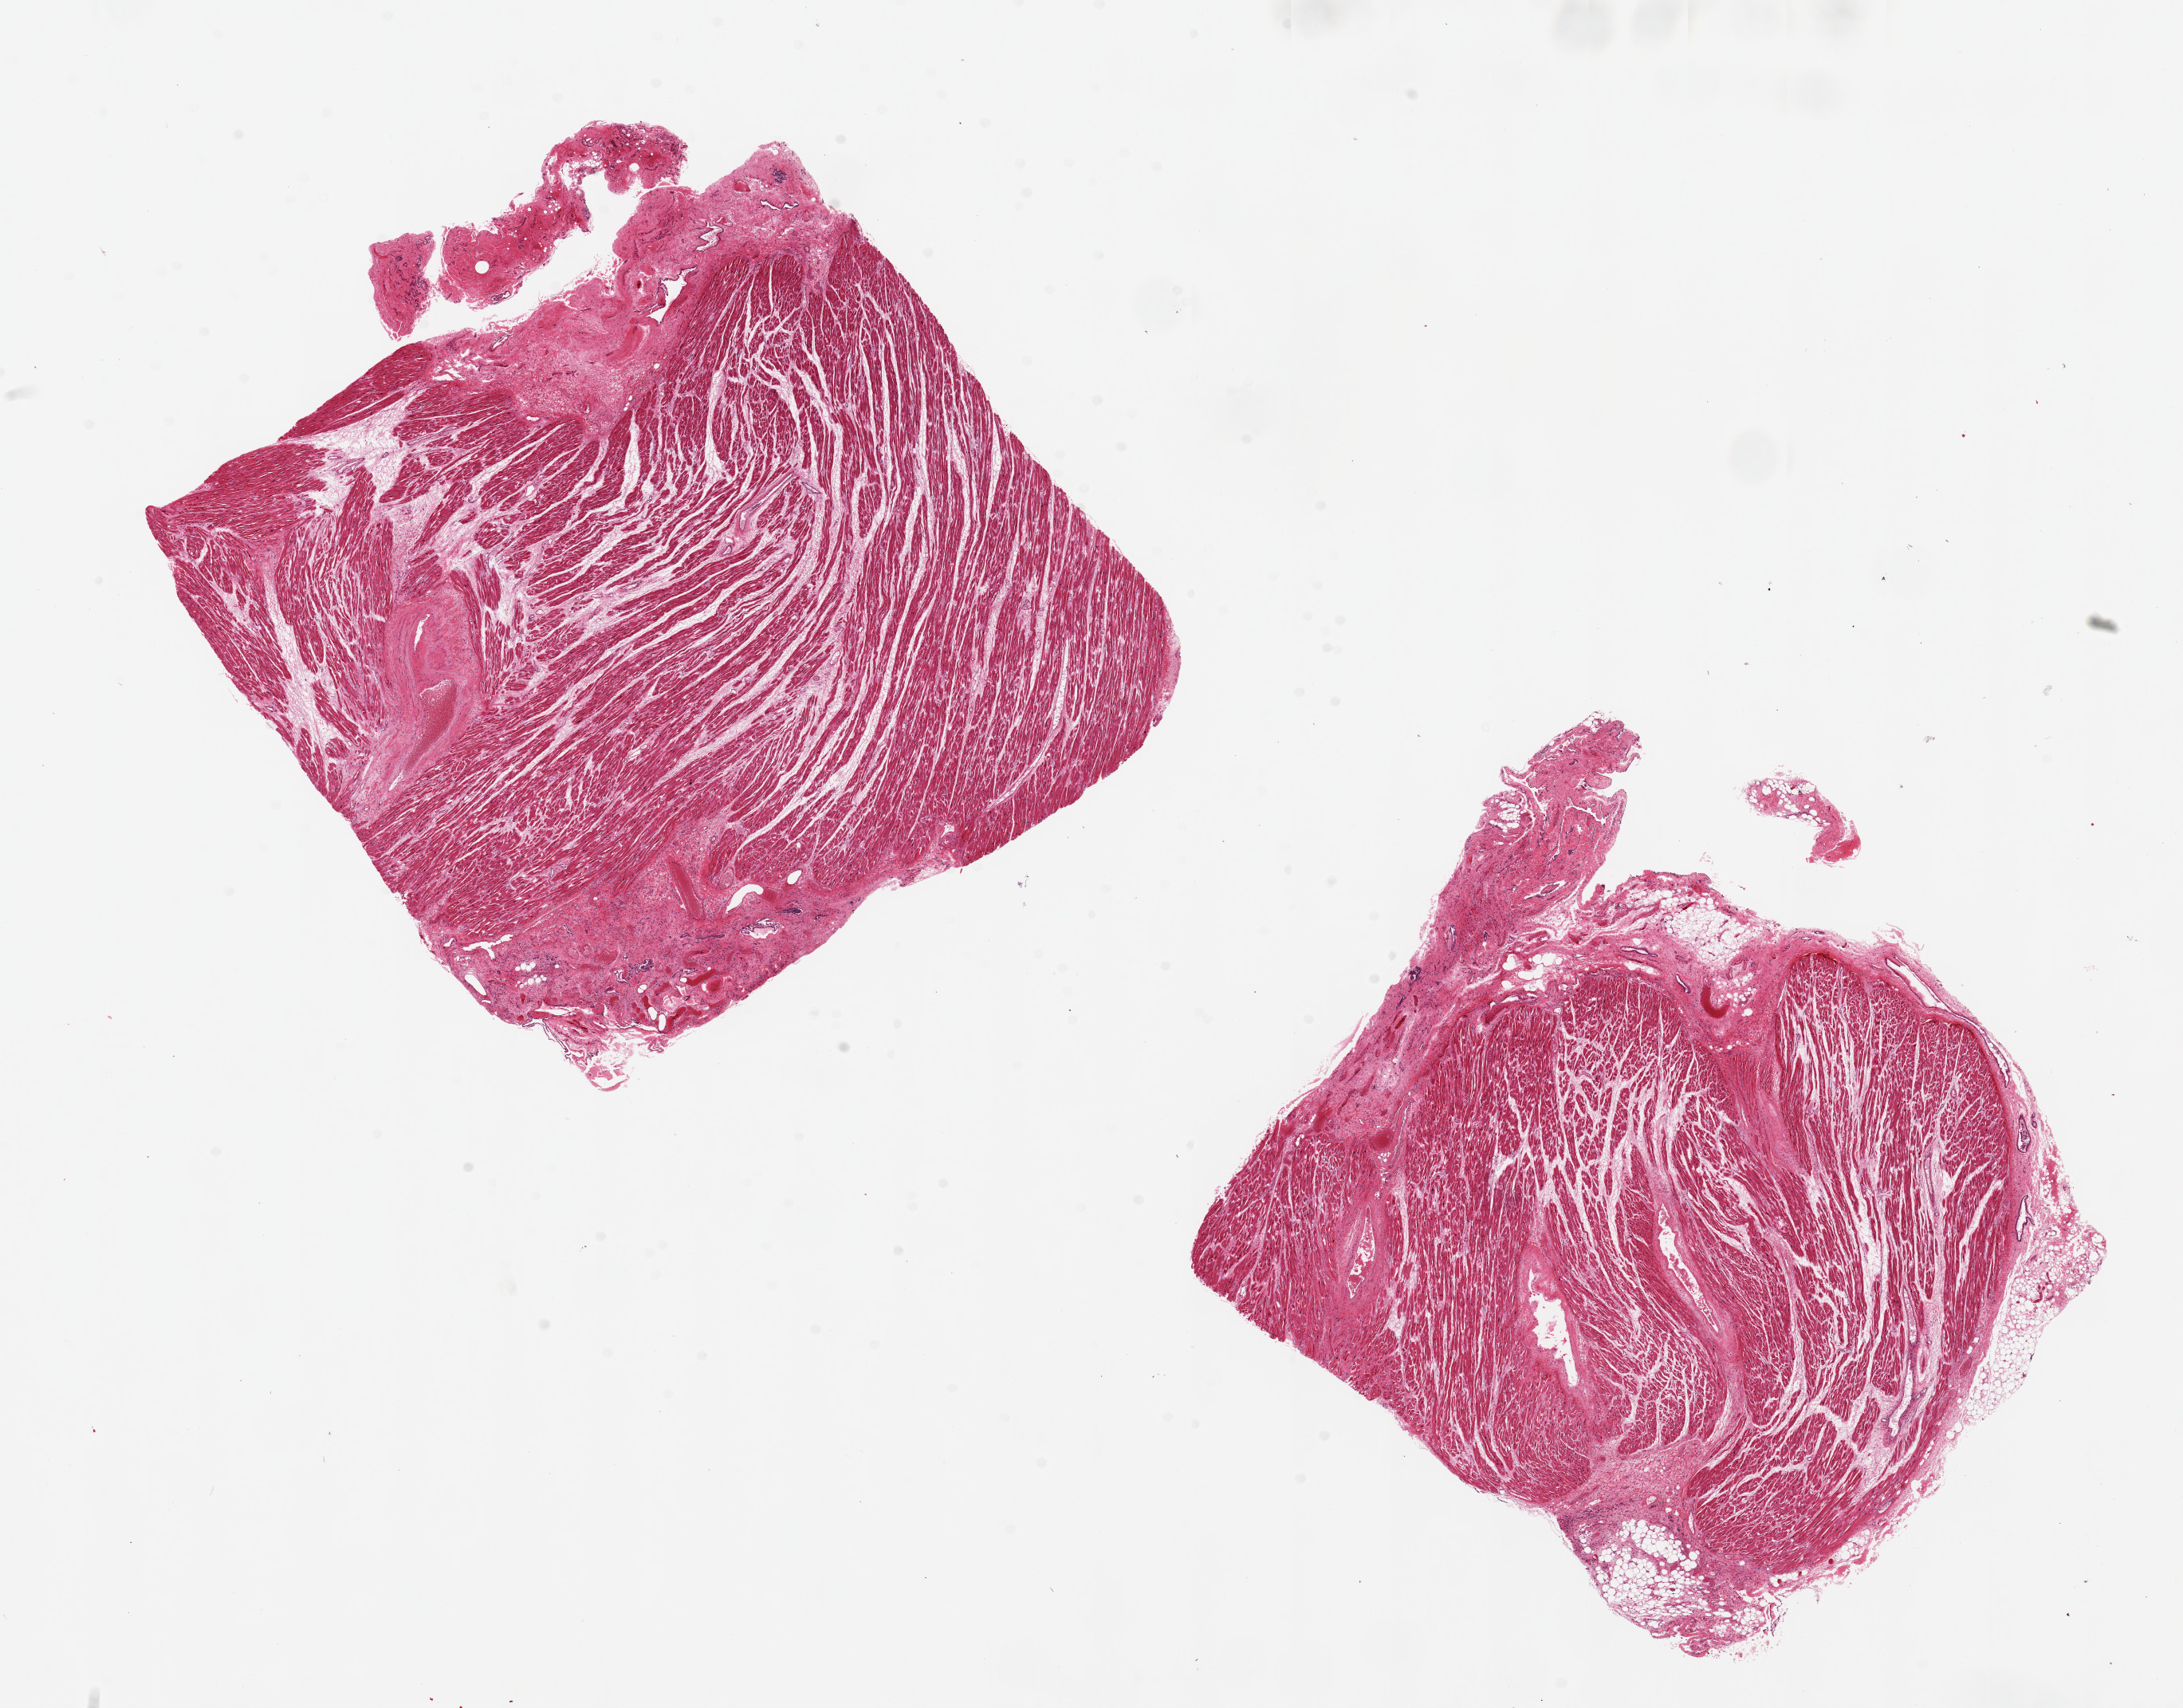
Hematoxylin and eosin (H&E) whole-slide image, whole scanned area (about 21.7 x 16.9 mm) shown as a low-resolution overview, PAXgene-fixed paraffin-embedded (PFPE) section, target tissue: auricular appendage, tissue donor sample. Male donor.
Pathologist's review note for this sample: 2 pieces, 8x7 & 7x7mm.